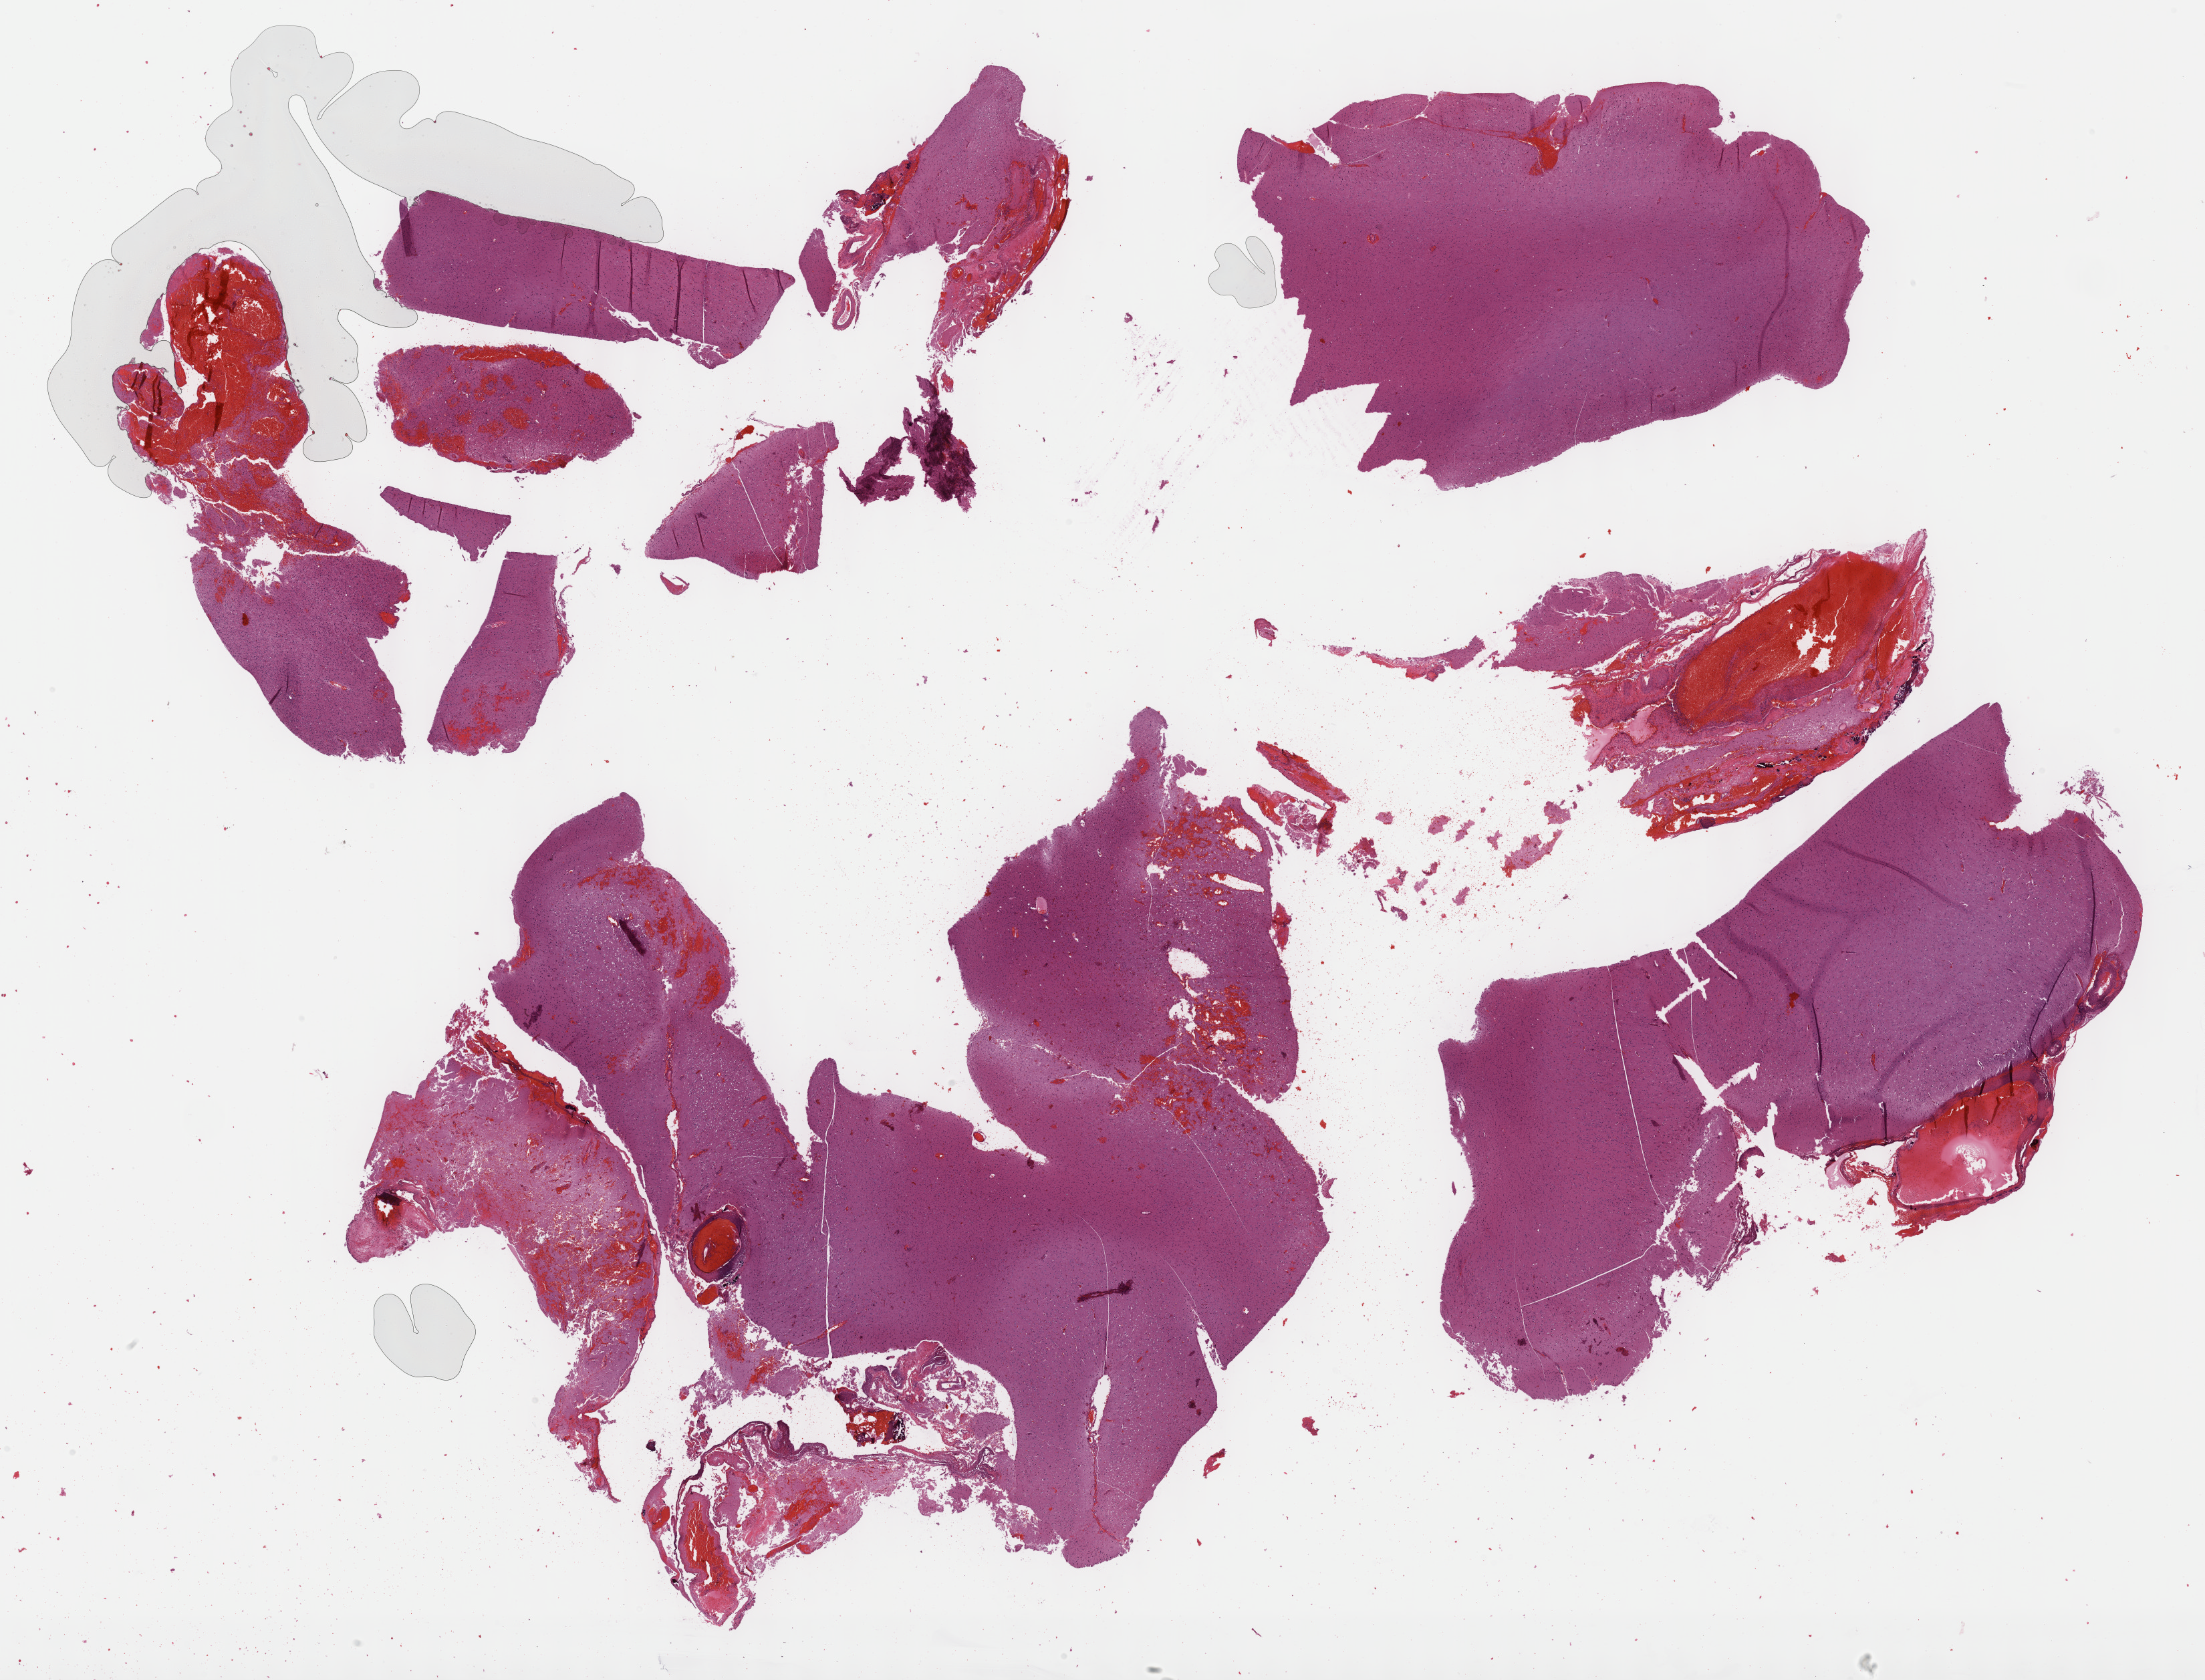
H&E-stained whole-slide image — shown as a low-resolution overview of the whole scanned area (about 26.7 x 20.3 mm, slide scanned at 40x); formalin-fixed paraffin-embedded (FFPE) diagnostic section; primary tumour sample from the brain. Patient: female, age at initial diagnosis 30 years.
Histologic diagnosis: Astrocytoma, NOS.